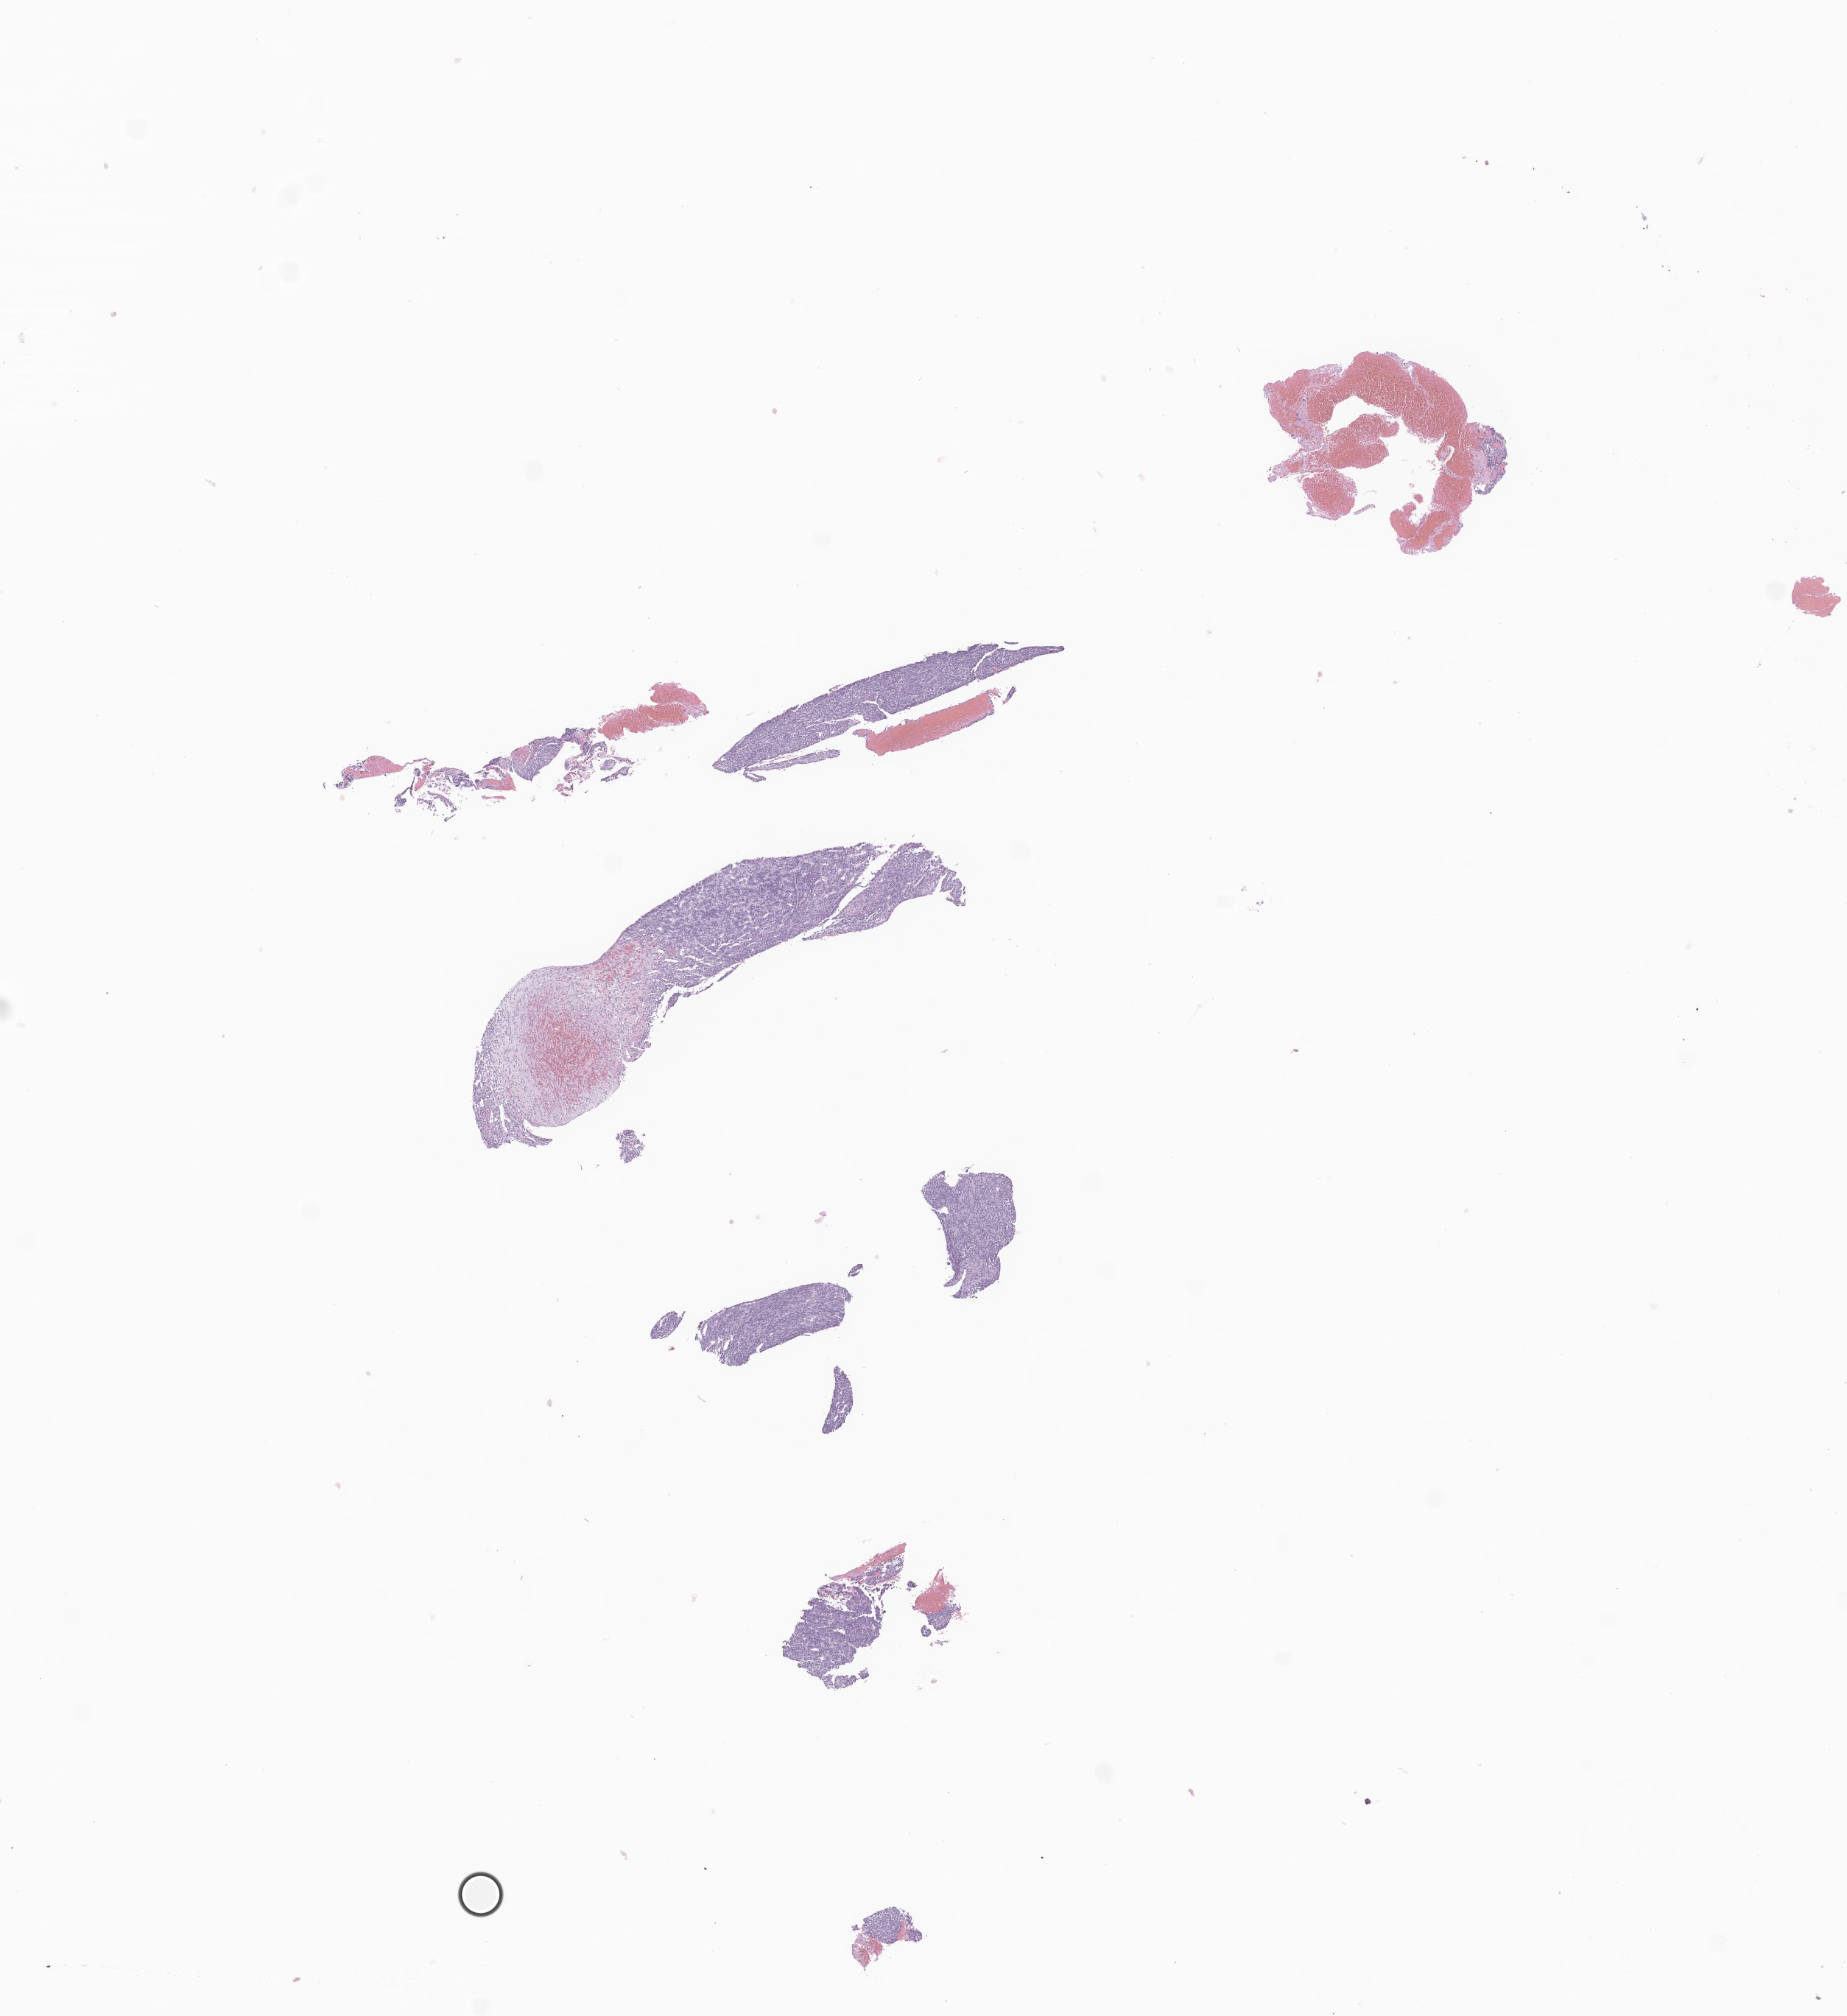
Digitized haematoxylin and eosin-stained section of tumor tissue from the soft tissue of lower extremity — low-resolution overview of the scanned area, about 10.6 x 11.5 mm; formalin-fixed, paraffin-embedded (FFPE) tissue. Male patient, age 168 months (14 years).
Diagnosis (ICD-O-3 morphology term): Synovial sarcoma, NOS.